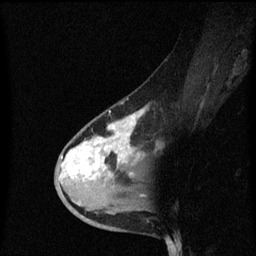
Breast MRI (dynamic contrast-enhanced), one sagittal slice. Position 34 of 60 along the scan axis. Dynamic contrast-enhanced series, image 2 of 3 at this slice position (ordered by acquisition). 1.5 T. TE 4.2 ms, TR 8.4 ms. 2 mm slice thickness. 256 × 256 image matrix, field of view 200 × 200 mm. Patient: female, 38 years. Case-level facts recorded for this patient, not image findings: setting: breast cancer imaged before/during neoadjuvant chemotherapy; receptor status: HR-positive, HER2-negative.
Structures marked on this image (semi-automatic segmentation, software-assisted and operator-edited):
- analysis volume of interest (the breast-tissue region the enhancement analysis was run in; not a lesion): box from (x=56, y=100) to (x=147, y=205) px
- tumour enhancement mask (voxels above the 70 % enhancement threshold inside the analysis volume of interest): (x=62, y=110)–(x=143, y=177)